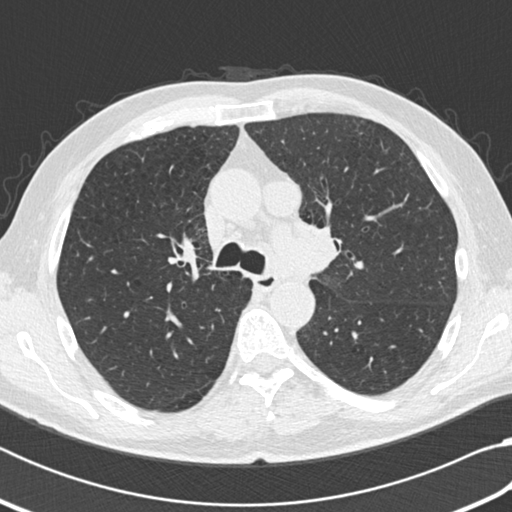
Low-dose screening chest CT, axial slice, third screening round (two years after baseline), lung window (W 1500 / L -600 HU), 120 kVp, slice 70 of 207 in the series. Male participant, aged 64 years at enrolment. Current smoker at enrolment.
Expert-annotated lung lesion, bounding box <252,176,297,218> (left, top, right, bottom; pixels). No non-calcified nodule or mass ≥4 mm was recorded by the screening reader at this exam. Official screen result: negative screen, significant abnormalities not suspicious for lung cancer. Participant outcome: lung cancer diagnosed 163 days after this screen — small cell carcinoma, NOS, mediastinum, stage IV (AJCC 6th edition).